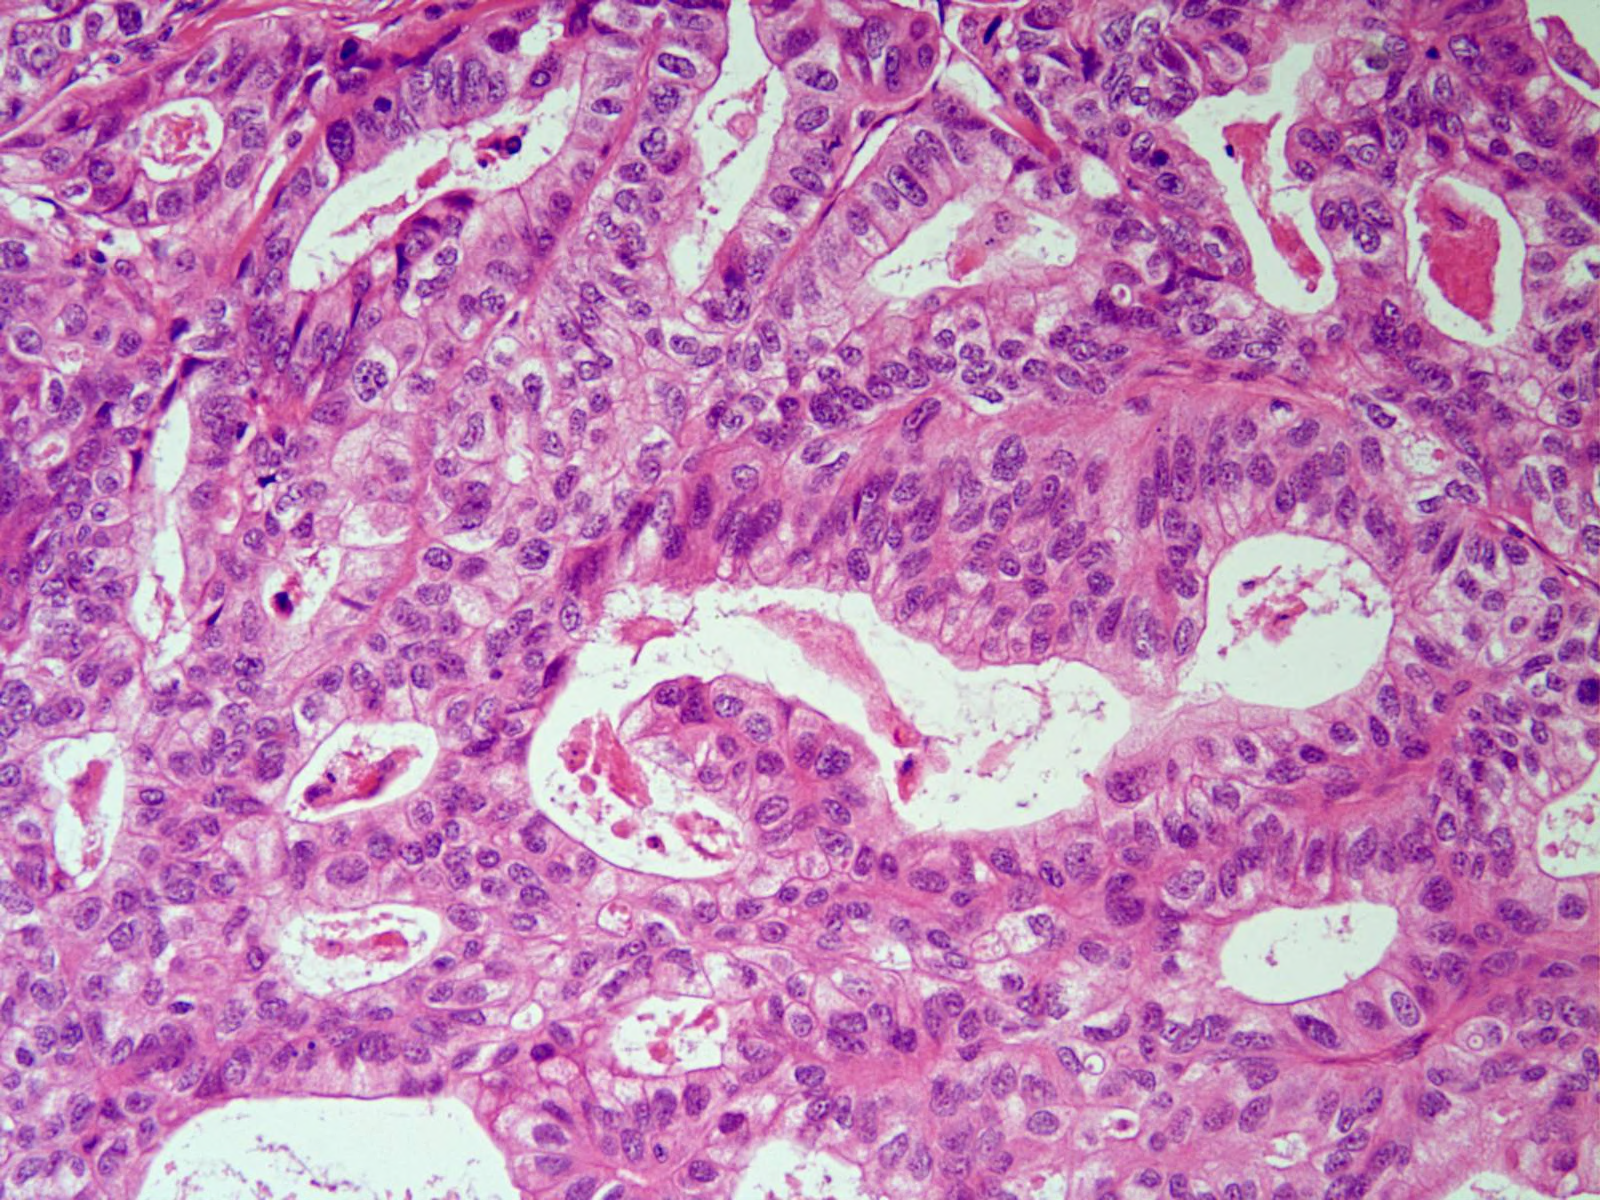
H&E image of one small field of the section — about 0.8 x 0.6 mm across, FFPE section, sample: primary tumour, stomach. Male patient; age at initial diagnosis 87 years. Histologic grade: G2 (moderately differentiated).
- histologic diagnosis: Adenocarcinoma, NOS